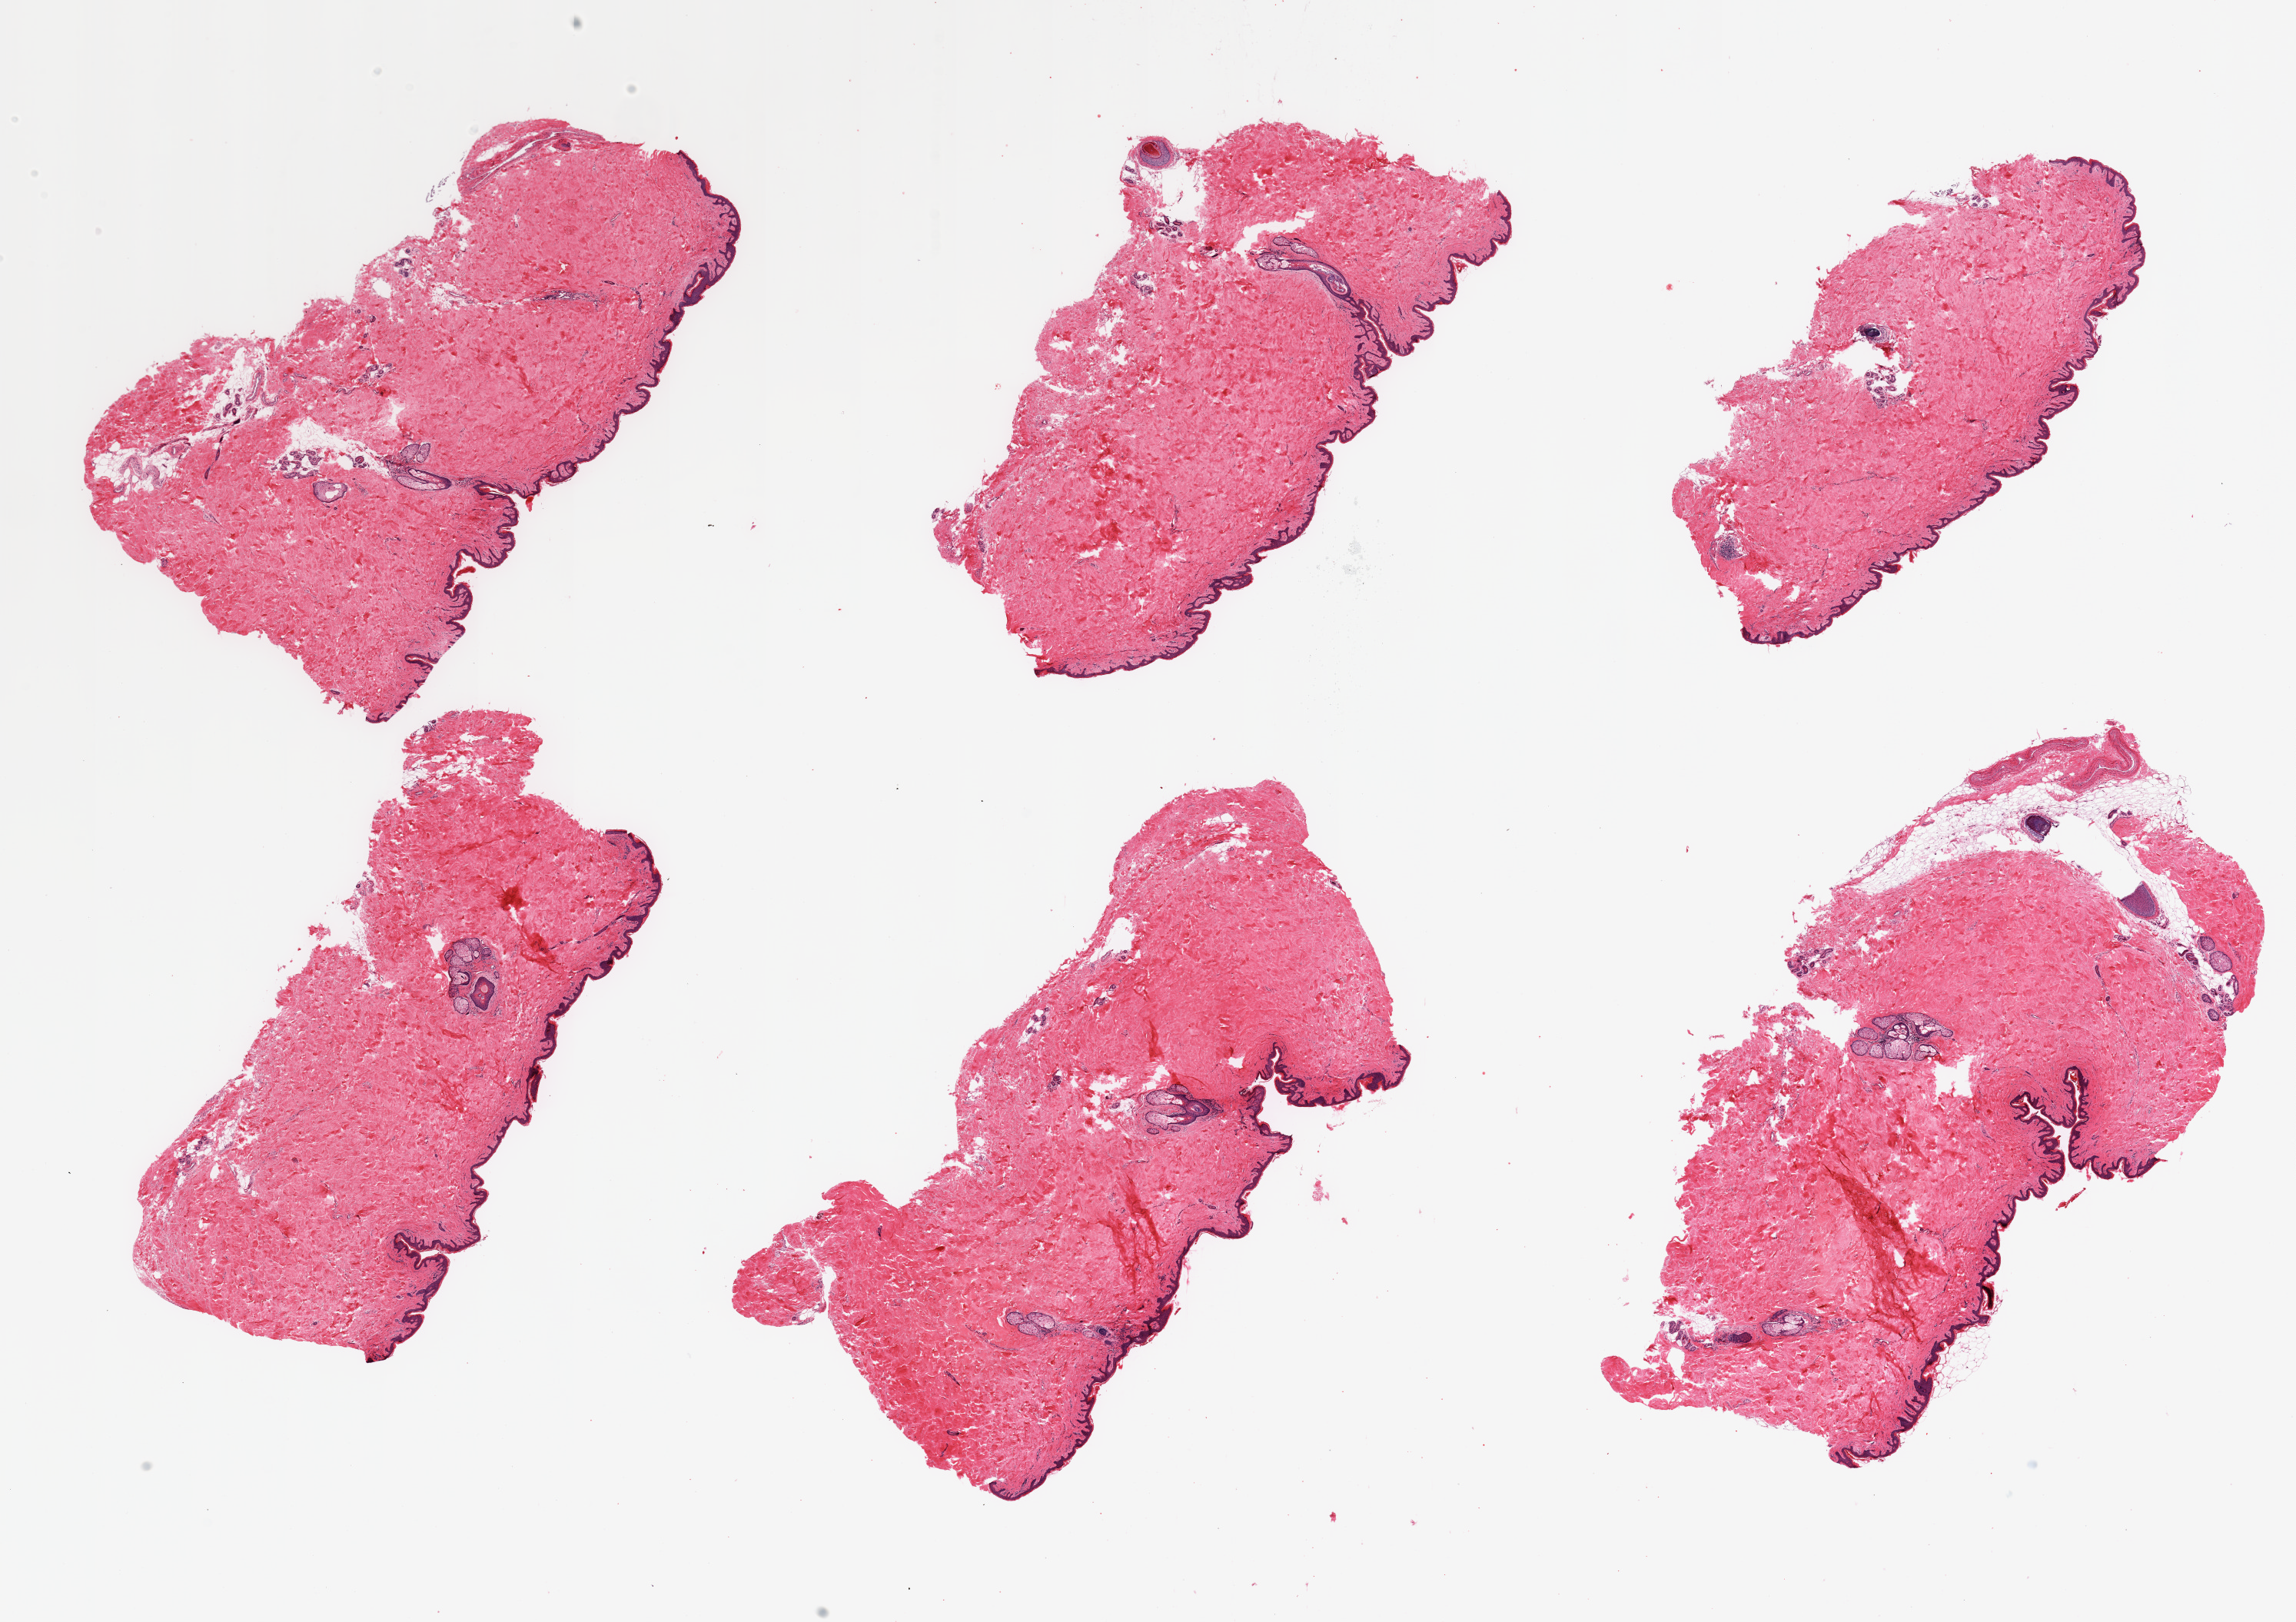
Digitized hematoxylin and eosin (H&E)-stained section — a low-resolution overview of the entire scanned area, about 23.6 x 16.7 mm, PAXgene-fixed, paraffin-embedded tissue, sampled site (target tissue): skin of suprapubic region, tissue donor sample. Donor: male.
* pathologist's review note for this sample: 6 pieces; well trimmed; up to 10% dermal fat